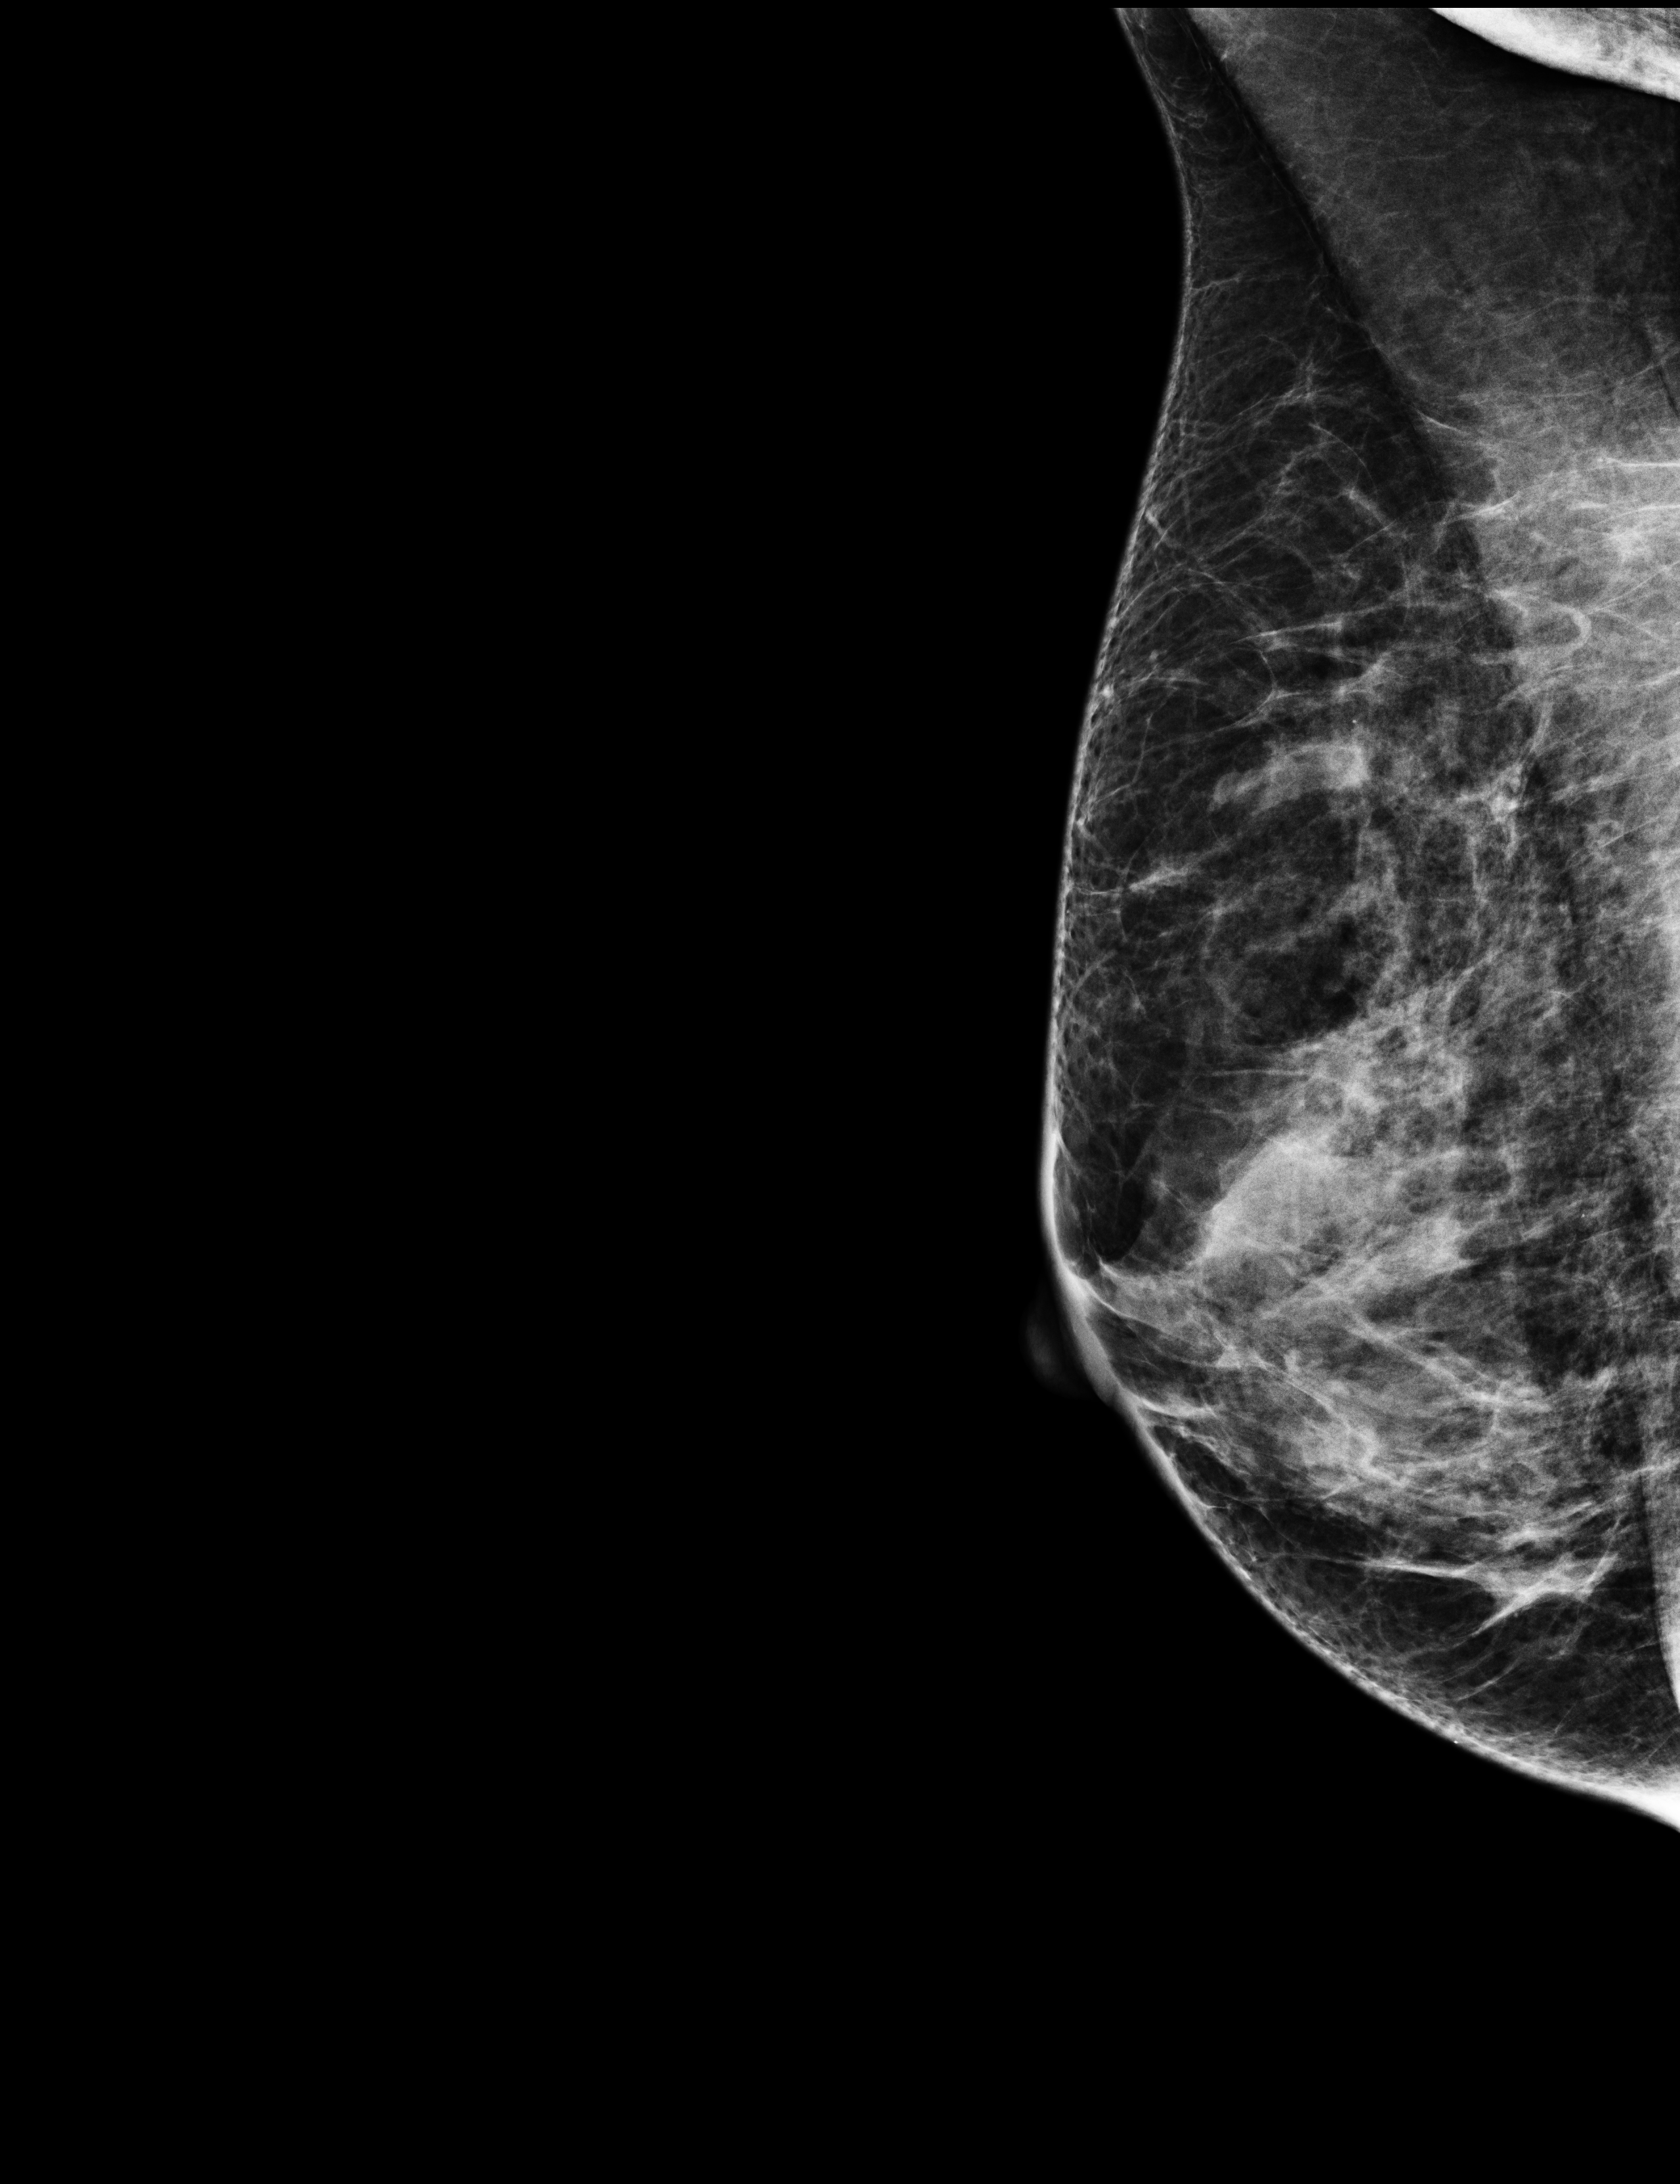
Screening examination, system: Selenia Dimensions. Patient aged 55 years (female).
Image type: full-field digital mammogram. Breast: right. Projection: MLO view. Breast density at the screening exam (both breasts): heterogeneously dense (BI-RADS density category c). Final BI-RADS assessment for this screening round (tomosynthesis exam, both breasts): category 1. Recall: no recall after this screen.